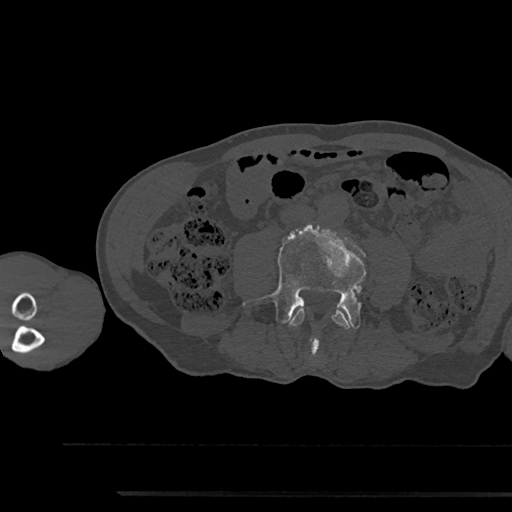
CT including the spine, one axial slice. Position 435 of 797 along the scan axis. 120 kVp. Bone window (W 1800 / L 400 HU). 512 × 512 image matrix, field of view 367 × 367 mm. Patient: male, 79 years. Case-level facts recorded for this patient, not image findings: primary cancer: prostate.
Annotated regions visible in this slice (semi-automatically segmented with operator editing):
- L3 vertebra: bounding box [x1, y1, x2, y2] px = [289, 307, 350, 330]
- L4 vertebra: [243, 225, 366, 354]